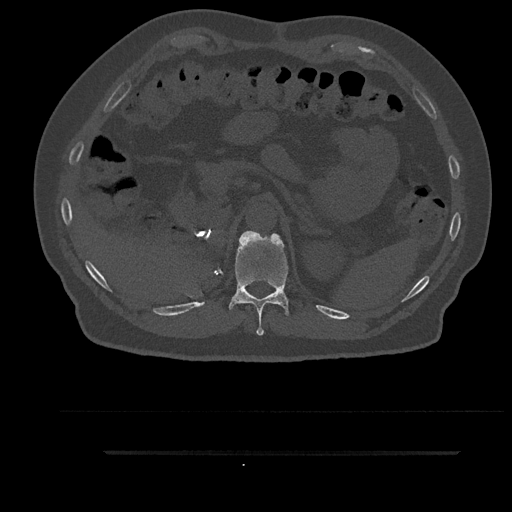
CT including the spine, one axial slice. Position 299 of 797 along the scan axis. Reconstruction kernel Br40s/3. 120 kVp. Bone window (W 1800 / L 400 HU). 0.5 mm slice thickness. 512 × 512 image matrix, field of view 432 × 432 mm. Male patient, age 63 years. From the clinical record (not read from this slice): primary cancer: renal.
Structures marked on this image (semi-automatic segmentation, software-assisted and operator-edited):
- T11 vertebra: bounding box <222,231,292,336> (left, top, right, bottom; pixels)